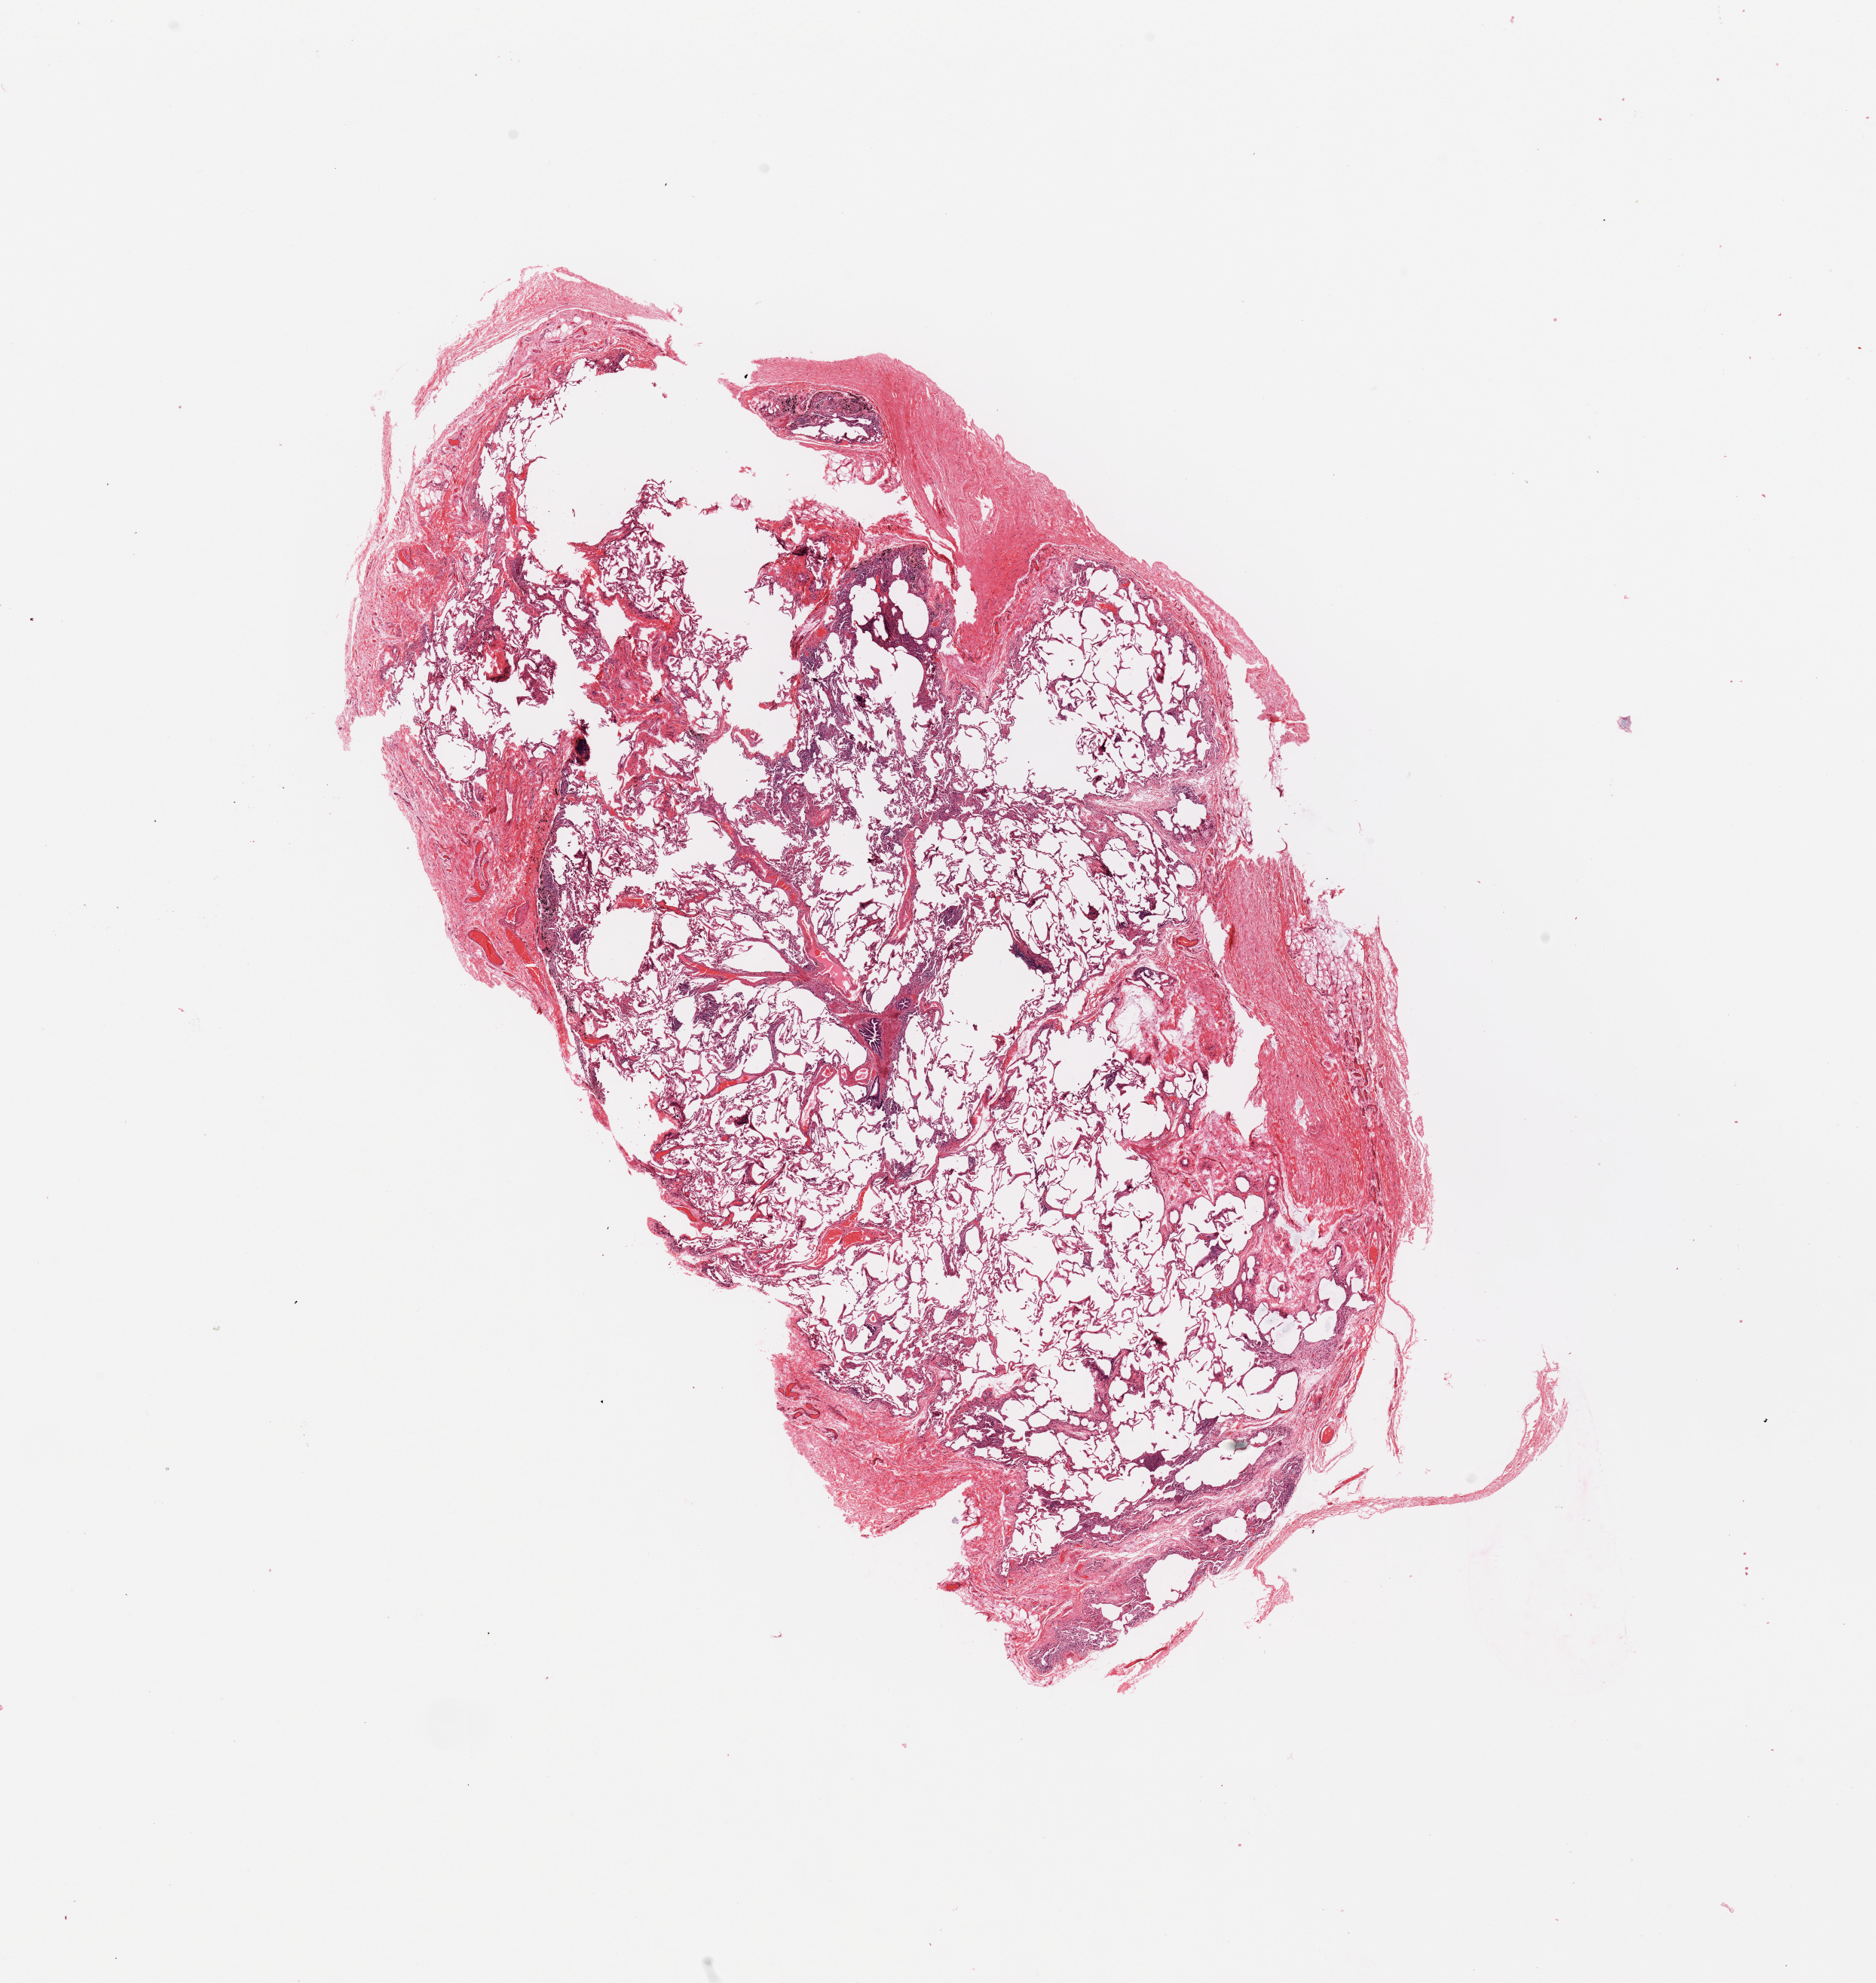
H&E whole-slide image, low-resolution overview of the scanned area, about 19.7 x 20.8 mm (slide scanned at 20x), normal (non-tumour) tissue sample, sampled site: lung. Male, 56 y/o.
- this section: normal (non-tumour) tissue from the same patient
- patient diagnosis: Adenocarcinoma, NOS